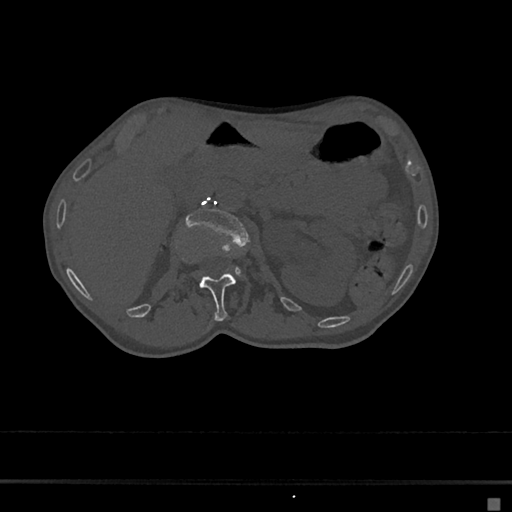
CT including the spine, one axial slice; position 55 of 797 along the scan axis; bone window (W 1800 / L 400 HU); 0.5 mm slice thickness; 512 × 512 image matrix, field of view 360 × 360 mm. Female patient, age 68 years. From the clinical record (not read from this slice): primary cancer: renal.
Structures marked on this image (semi-automatic segmentation, software-assisted and operator-edited):
- L1 vertebra: bounding box <186,256,236,321> (left, top, right, bottom; pixels)
- L2 vertebra: <187,207,248,273>